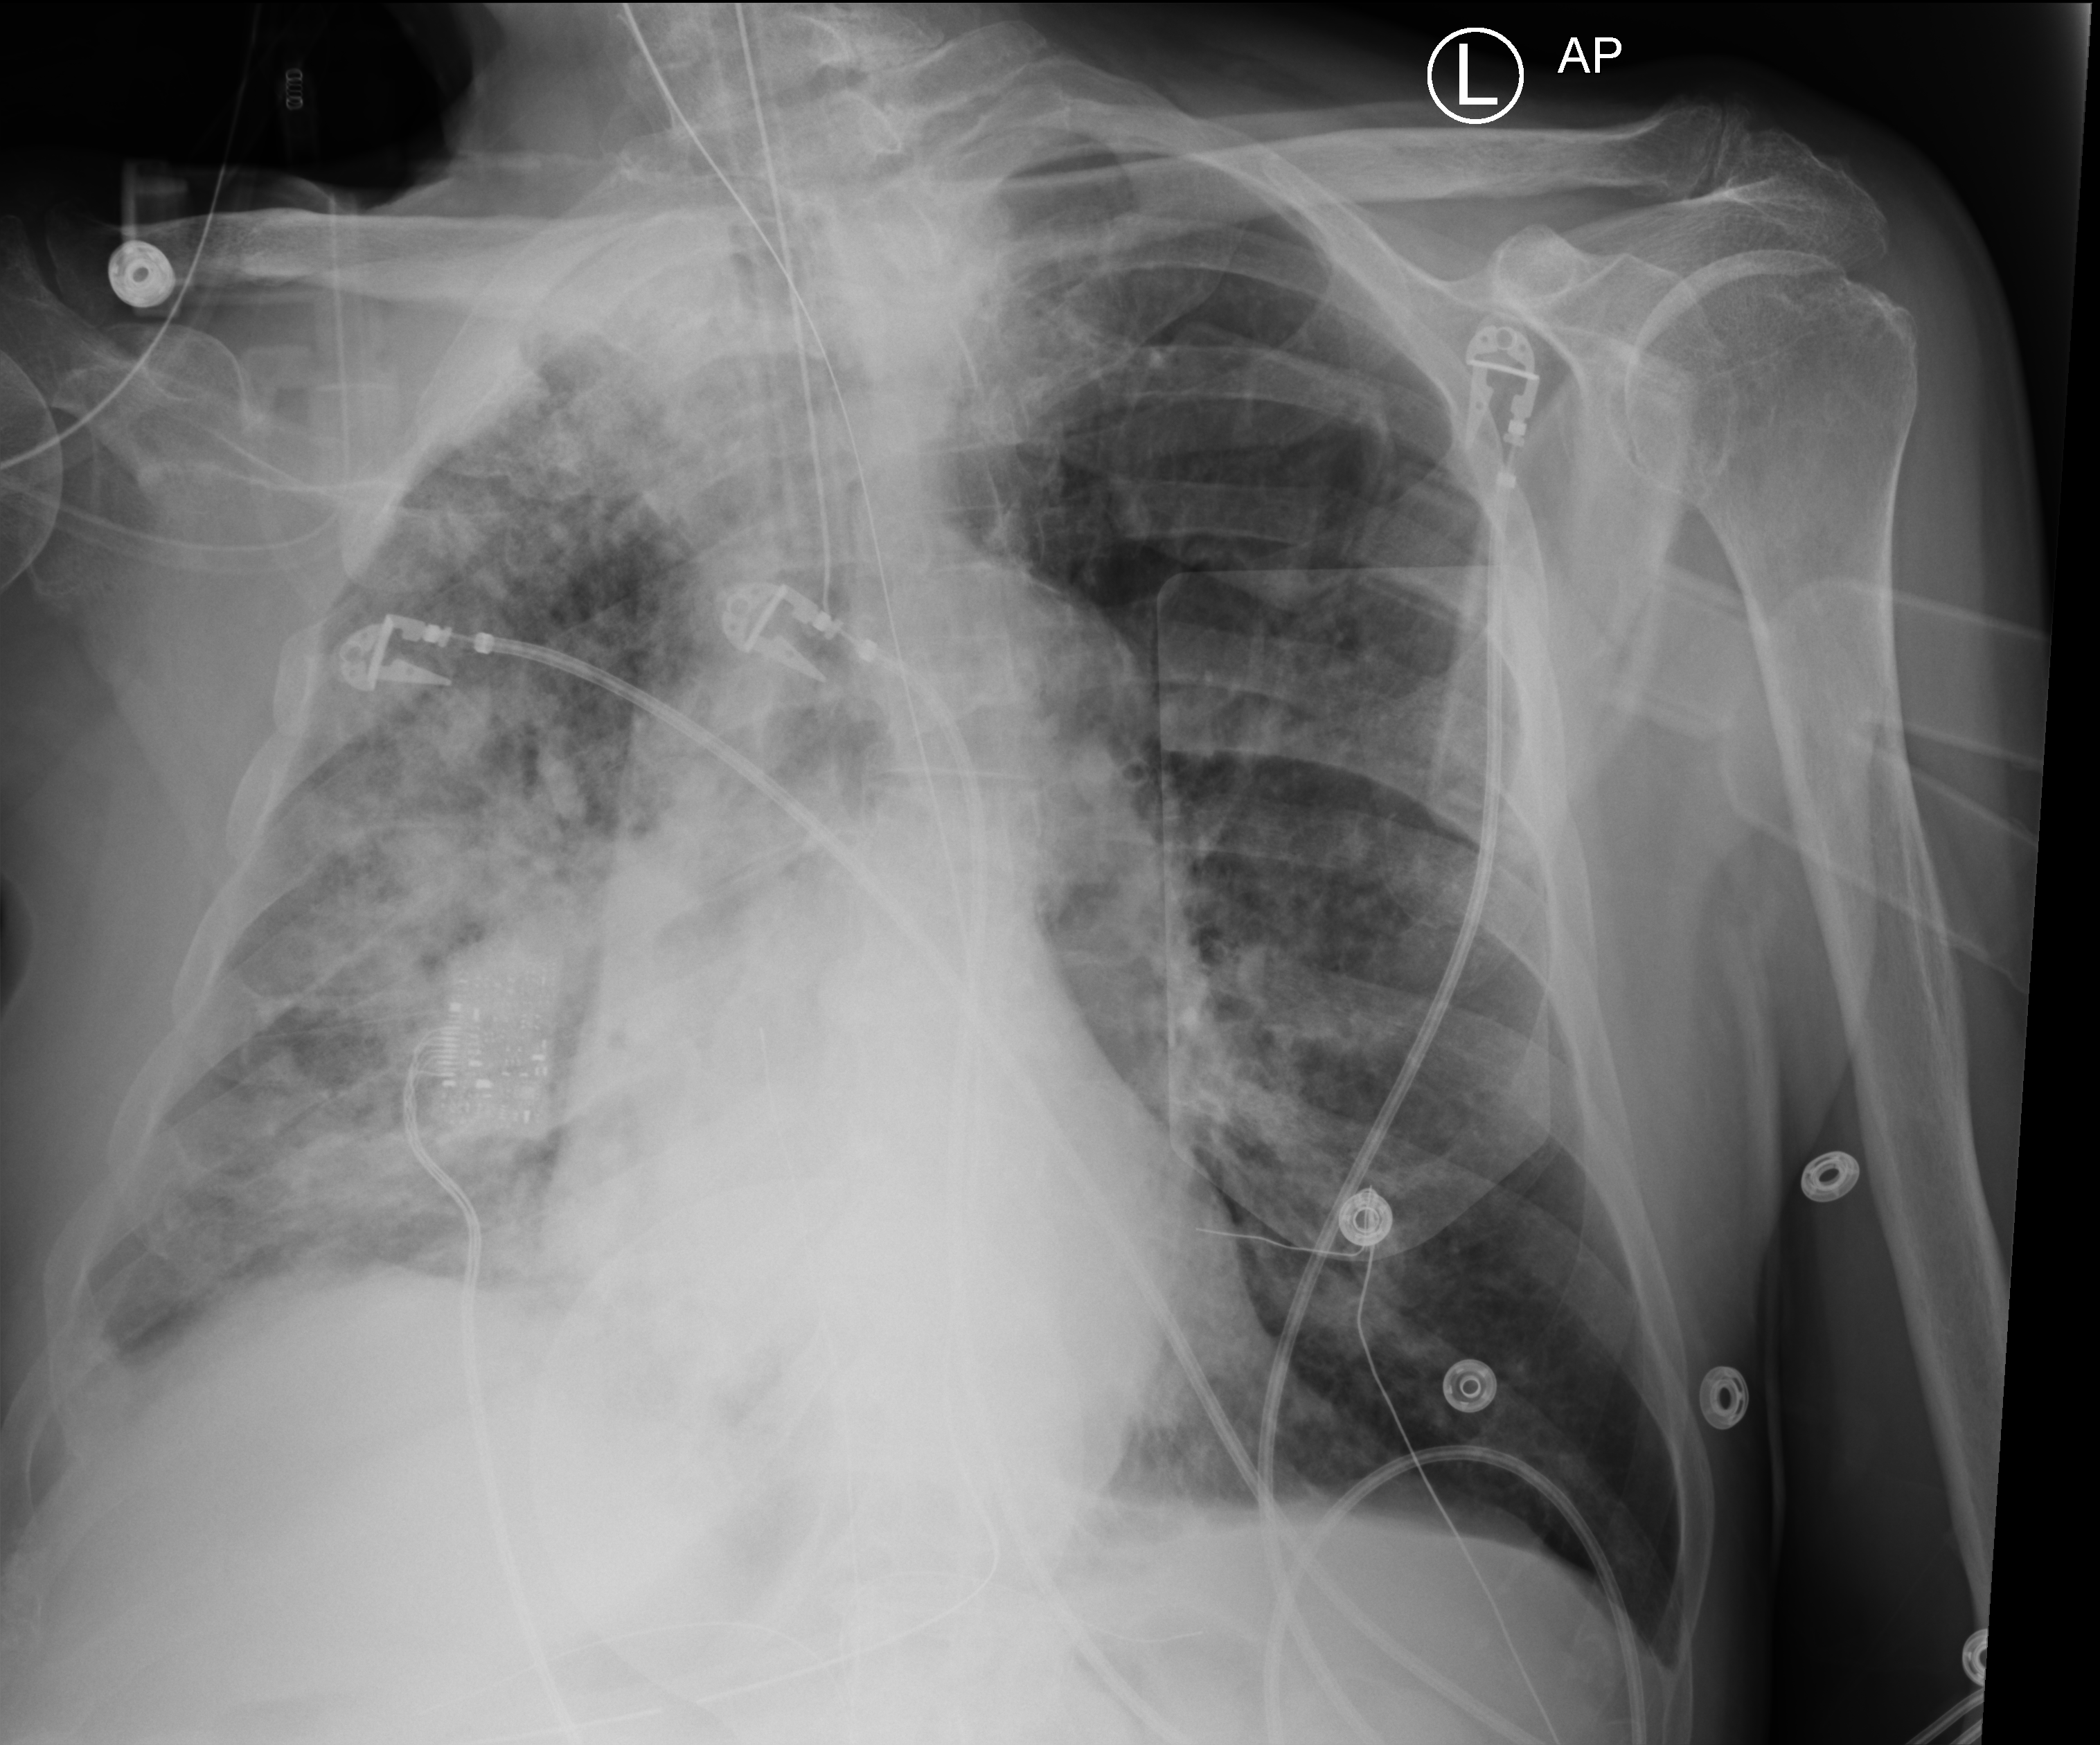
Portable chest radiograph; anteroposterior (AP) projection. Male patient hospitalised with COVID-19, age 75–90 years.
From the hospital-stay record, not from the radiograph (when in the stay this image was taken is not recorded):
- hypertension (admission record): yes